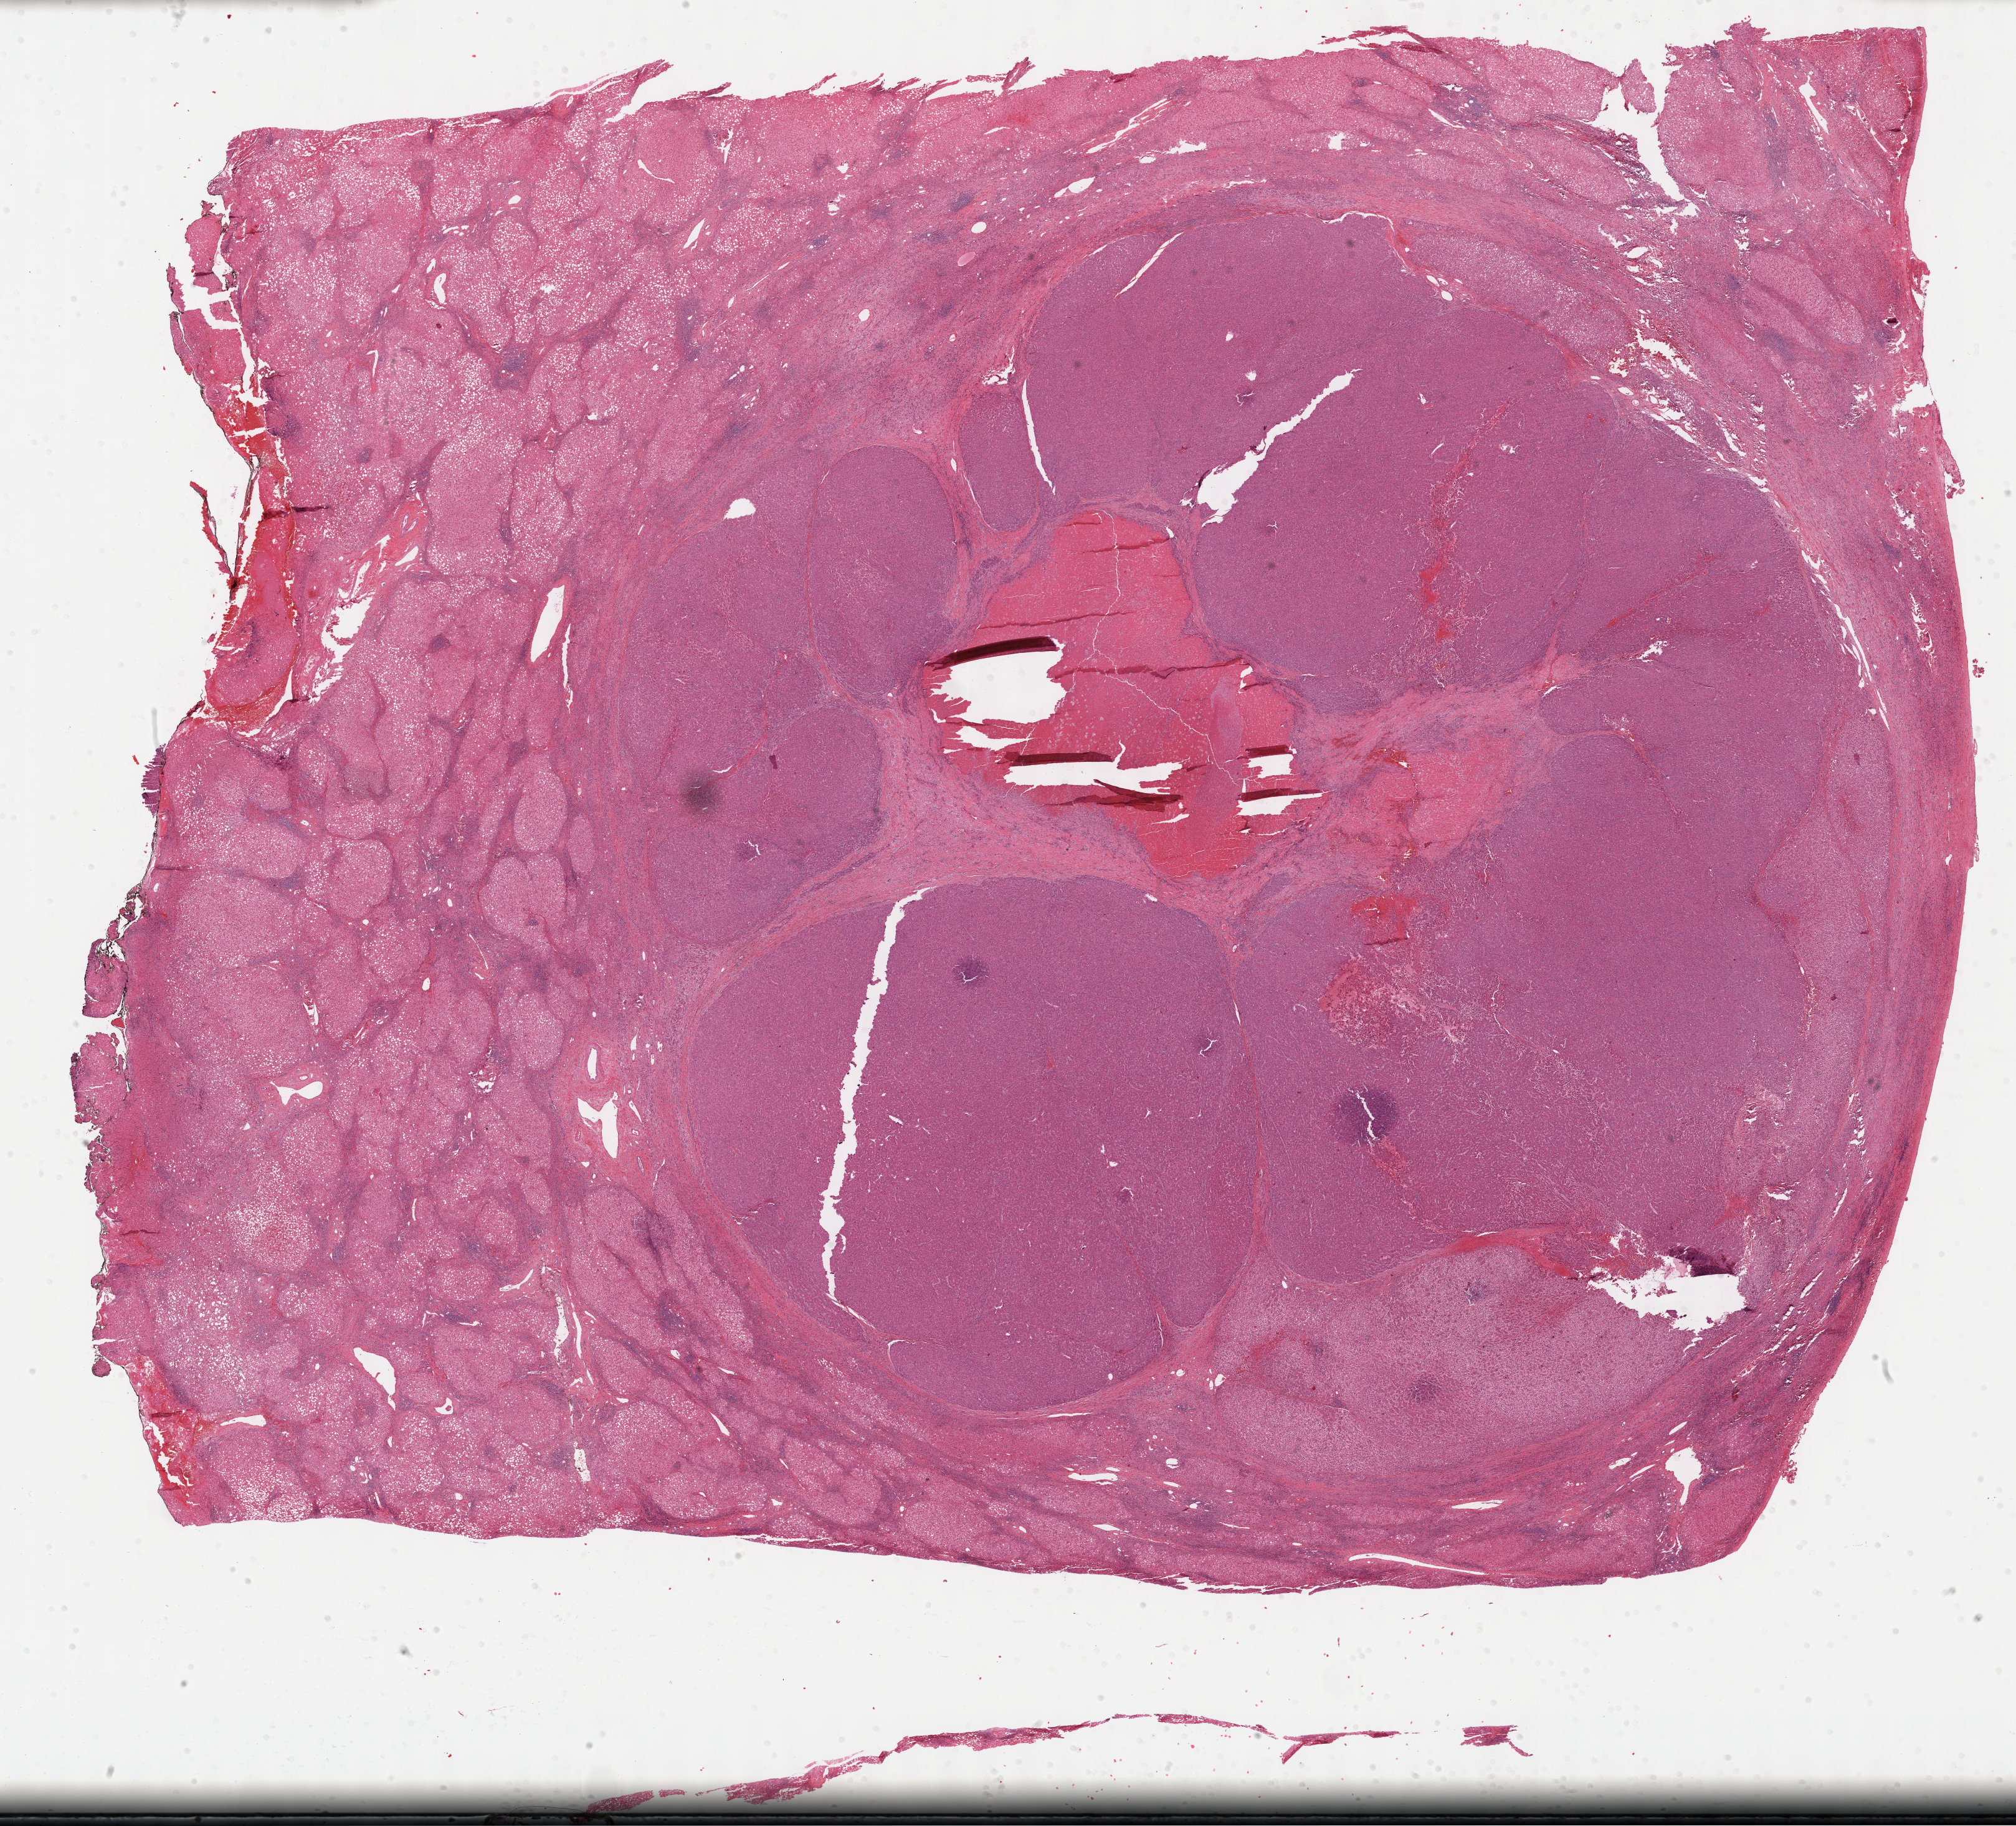
Whole-slide histology image, Hematoxylin and eosin (H&E) stained, a low-resolution overview of the entire scanned area, about 26.2 x 23.7 mm, formalin-fixed paraffin-embedded (FFPE) diagnostic section, liver, primary tumour sample. Male patient; age at initial diagnosis 59 years. Histologic grade: G1 (well differentiated).
Pathologic diagnosis: Hepatocellular carcinoma, NOS.